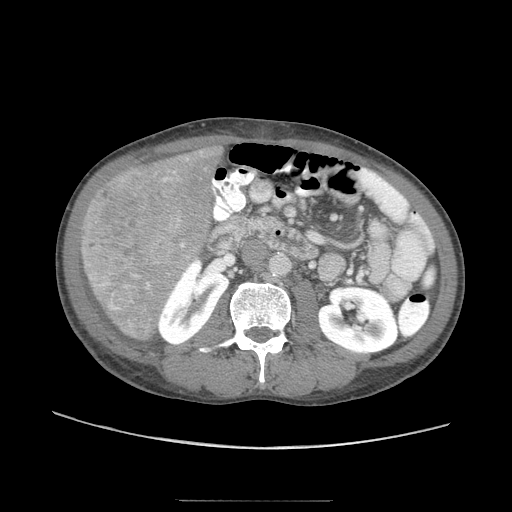
Contrast-enhanced abdominal CT (liver protocol), one axial slice. Position 20 of 103 along the scan axis. Soft-tissue window (W 400 / L 40 HU). 2.5 mm slice thickness. 512 × 512 image matrix, field of view 380 × 380 mm. From the clinical record (not read from this slice): diagnosis: hepatocellular carcinoma (patient treated with transarterial chemoembolisation; whether this scan precedes or follows treatment is not stated here); TNM stage (as recorded): Stage-IIIA; Child-Pugh class: A; tumour differentiation: moderately differentiated; tumour size: 16 cm.
Outlined on this slice (semi-automatic segmentation, software-assisted and operator-edited):
- liver parenchyma outside the tumour (the mass and vessels are separate outlines, so this box may not span the whole liver): bounding box (x1, y1, x2, y2) in pixels: (84, 144, 223, 340)
- mass: (79, 164, 191, 312)